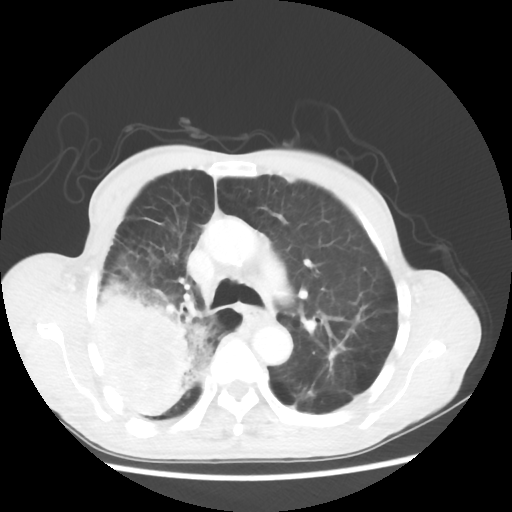
Chest CT, one axial slice. Slice 37 of 58 in the series (ordered by position). Reconstruction kernel STANDARD. 100 kVp. Lung window (W 1500 / L -600 HU). 5 mm slice thickness. 512 × 512 image matrix, field of view 351 × 351 mm. Patient: male, 75 years. From the clinical record (not read from this slice): clinical TNM (as recorded): T4 N1 M1.
Outlined on this slice (bounding box drawn by a radiologist):
- lung tumour (recorded histology: adenocarcinoma): bounding box (x1, y1, x2, y2) in pixels: (89, 267, 215, 418)